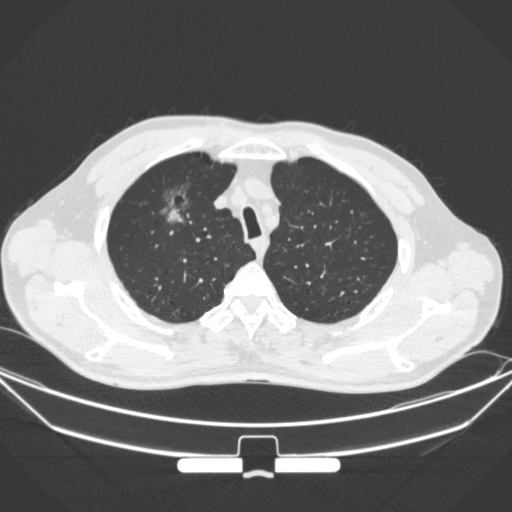
Chest CT, one axial slice. Slice 283 of 355 in the series (ordered by position). Lung window (W 1500 / L -600 HU). 1 mm slice thickness. 512 × 512 image matrix, field of view 399 × 399 mm. Male patient, age 67 years. Case-level facts recorded for this patient, not image findings: clinical TNM (as recorded): T1c N0 M0; histopathological grade: G2.
Annotated regions visible in this slice (bounding box drawn by a radiologist):
- lung tumour (recorded histology: adenocarcinoma): bounding box [x1, y1, x2, y2] px = [148, 176, 193, 235]